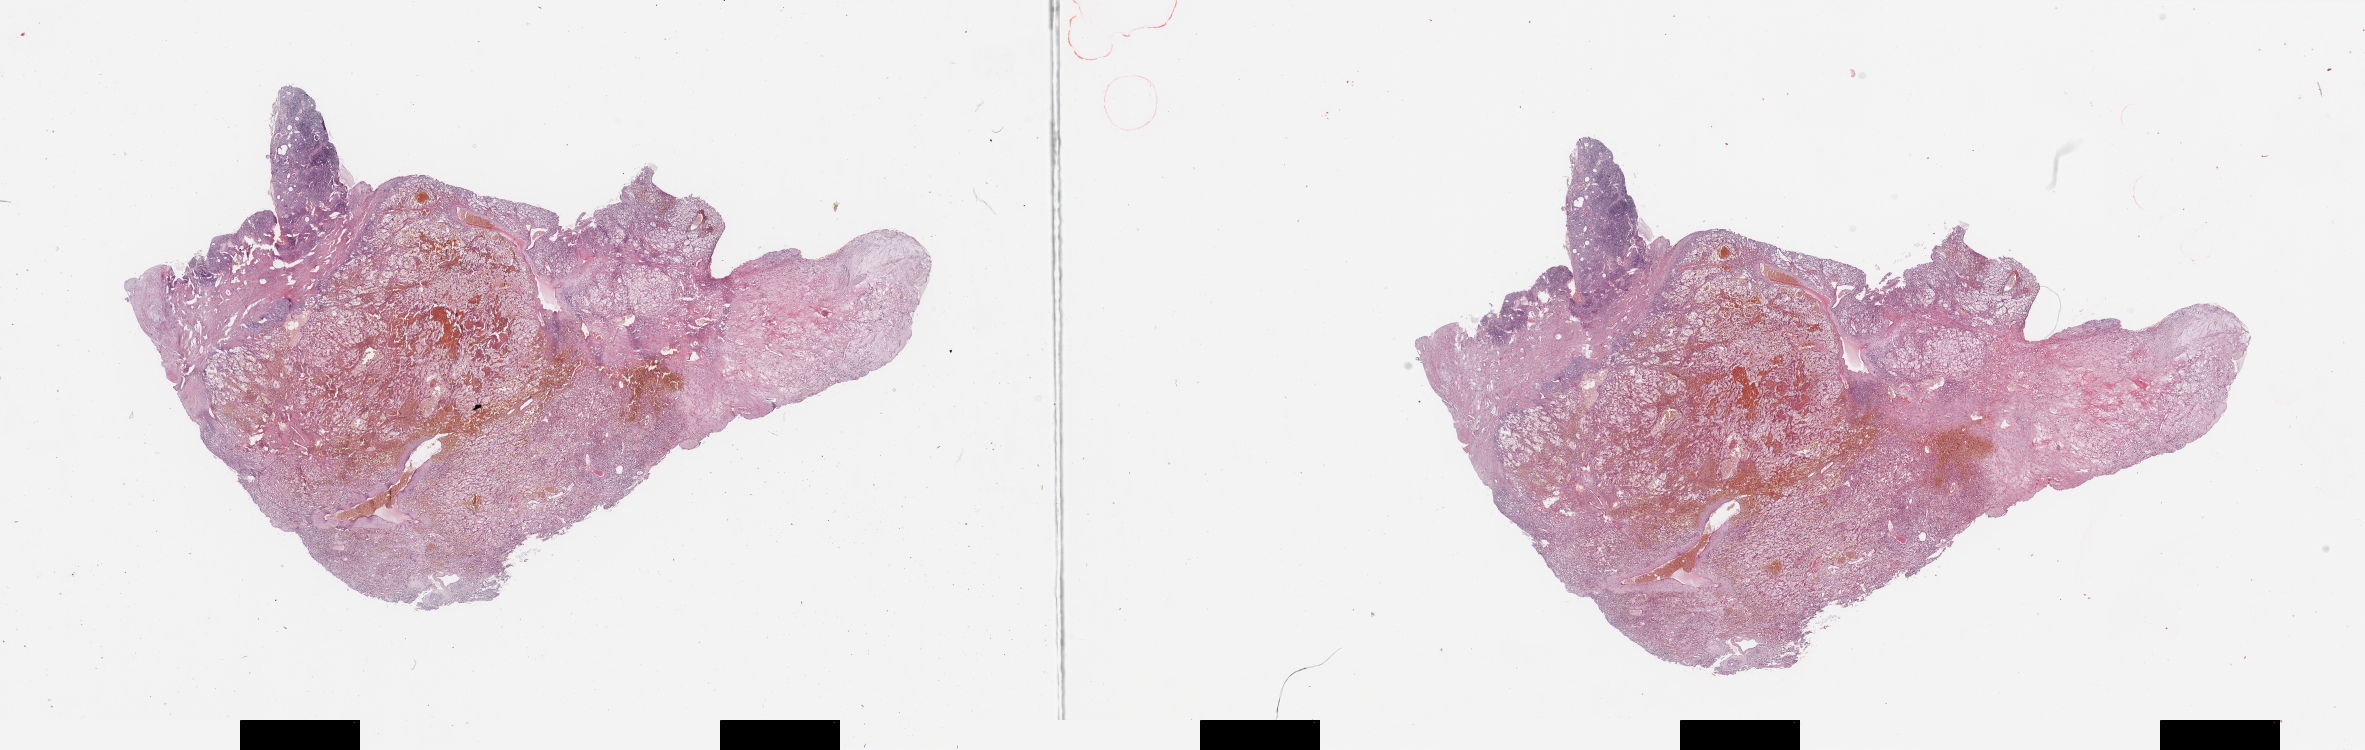
Whole-slide histology image, Hematoxylin and eosin (H&E) stained, whole scanned area (about 37.4 x 11.9 mm, slide scanned at 20x) shown as a low-resolution overview. Kidney, tumour tissue. Patient: male, age 53 years. Histologic grade: G3 (poorly differentiated).
Primary tumour site (as recorded): upper pole. Diagnosis: Renal cell carcinoma, NOS. AJCC pathologic stage: IV.